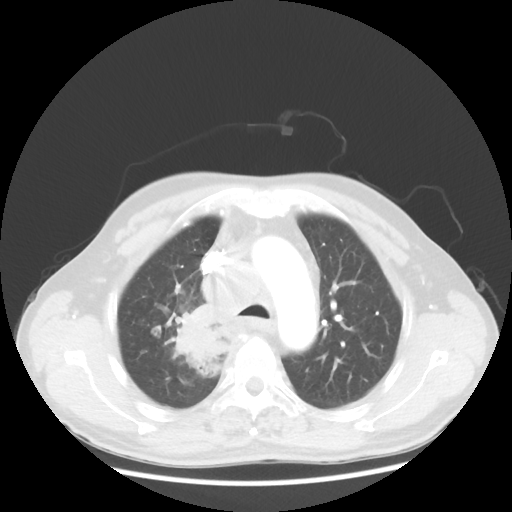
Chest CT, one axial slice; position 91 of 124 along the scan axis; 100 kVp; lung window (W 1500 / L -600 HU); 5 mm slice thickness; 512 × 512 image matrix, field of view 382 × 382 mm. Male patient, age 64 years. From the clinical record (not read from this slice): clinical TNM (as recorded): T3 N3 M0; histopathological grade: G3.
Outlined on this slice (bounding box drawn by a radiologist):
- lung tumour (recorded histology: small cell carcinoma): box from (x=166, y=295) to (x=234, y=383) px